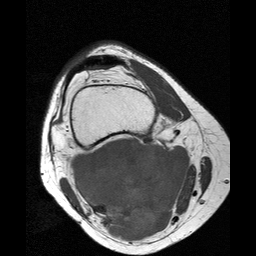
MRI of an extremity soft-tissue mass, one axial slice; position 16 of 25 along the scan axis; 256 × 256 image matrix, field of view 160 × 160 mm. Female patient. Case-level facts recorded for this patient, not image findings: histological type: liposarcoma; site of the primary tumour: right thigh.
Structures marked on this image (expert manual segmentation):
- gross tumour volume (mass): bounding box <70,139,190,241> (left, top, right, bottom; pixels)